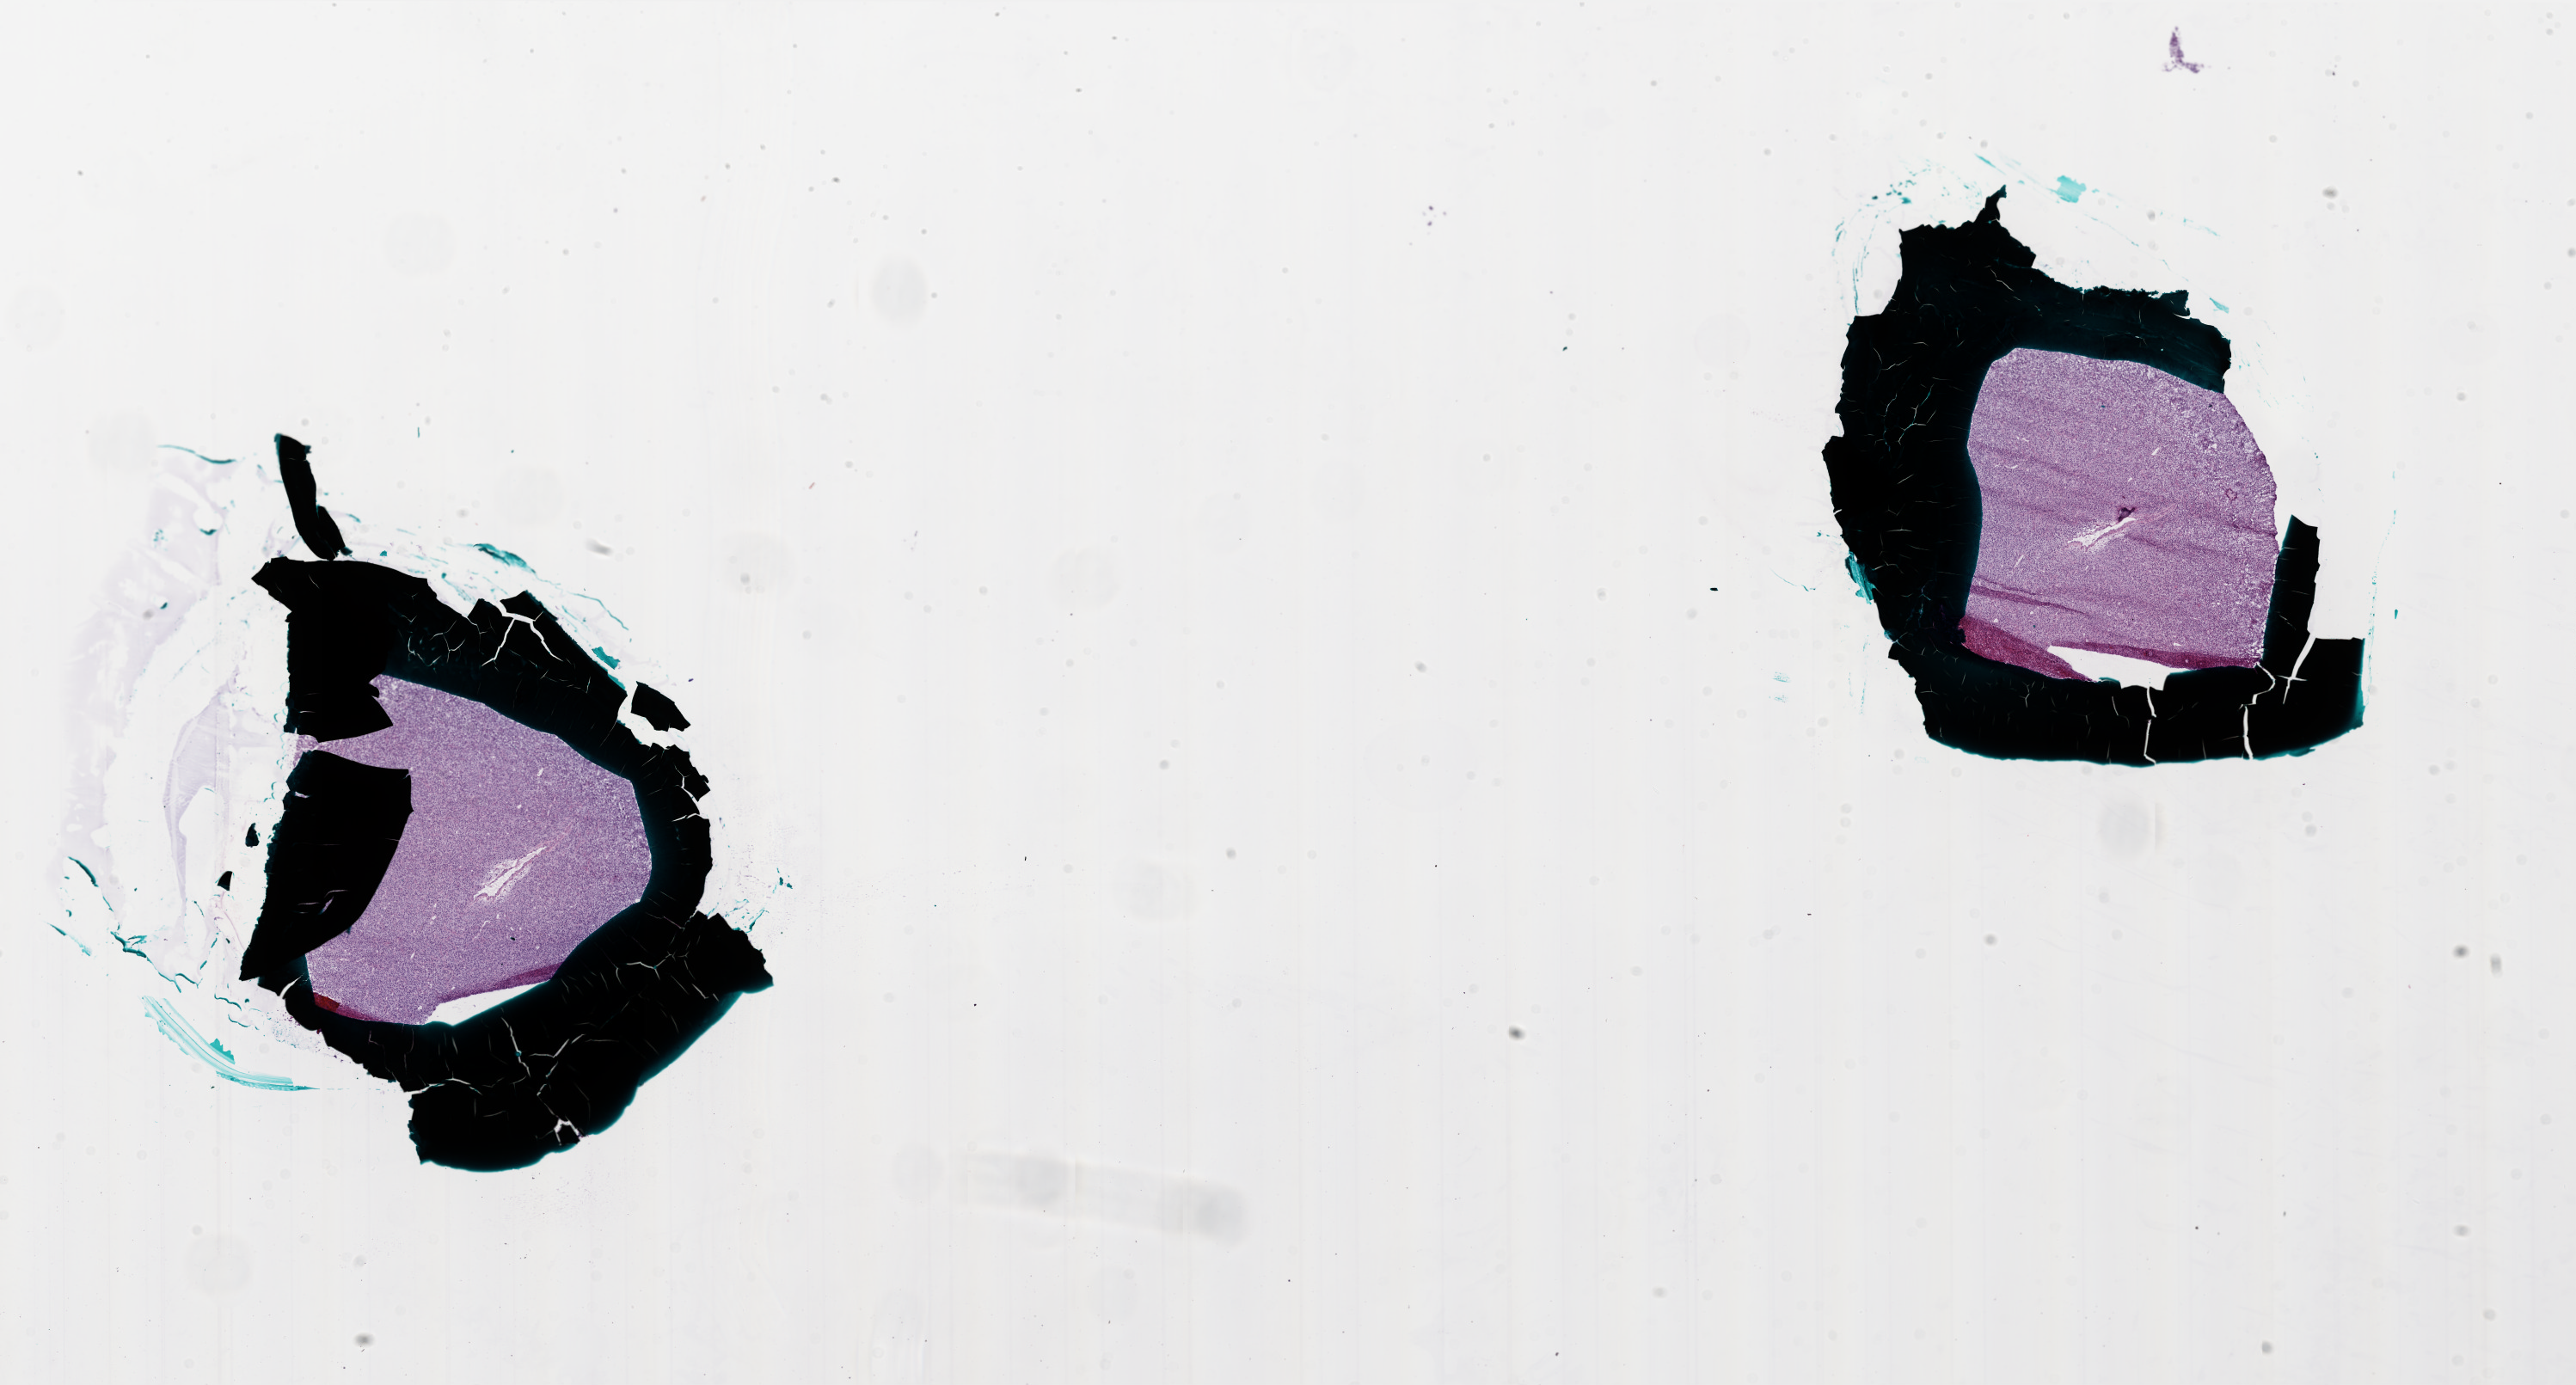
Whole-slide histology image, Hematoxylin and eosin (H&E) stained, a low-resolution overview of the entire scanned area, about 24.0 x 12.9 mm (from a 20x scan), frozen section from the bottom of the tissue portion, primary tumour sample from the brain. Male patient; age at initial diagnosis 47 years. Slide review estimates, as recorded: tumour cells 100%, tumour nuclei 95%, normal cells 0%, stromal cells 0%, necrosis 0%.
Diagnosis: Glioblastoma.